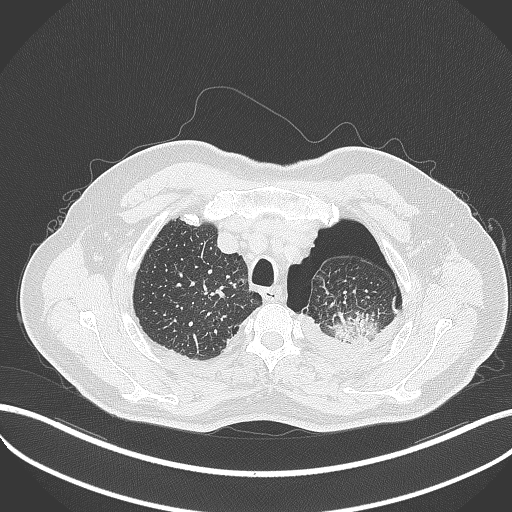
Chest CT, one axial slice. Position 418 of 464 along the scan axis. 120 kVp. Lung window (W 1500 / L -600 HU). 512 × 512 image matrix, field of view 400 × 400 mm. Male patient, age 76 years. From the clinical record (not read from this slice): clinical TNM (as recorded): T3 N0 M1b.
Structures marked on this image (bounding box drawn by a radiologist):
- lung tumour (recorded histology: adenocarcinoma): box from (x=326, y=305) to (x=381, y=349) px